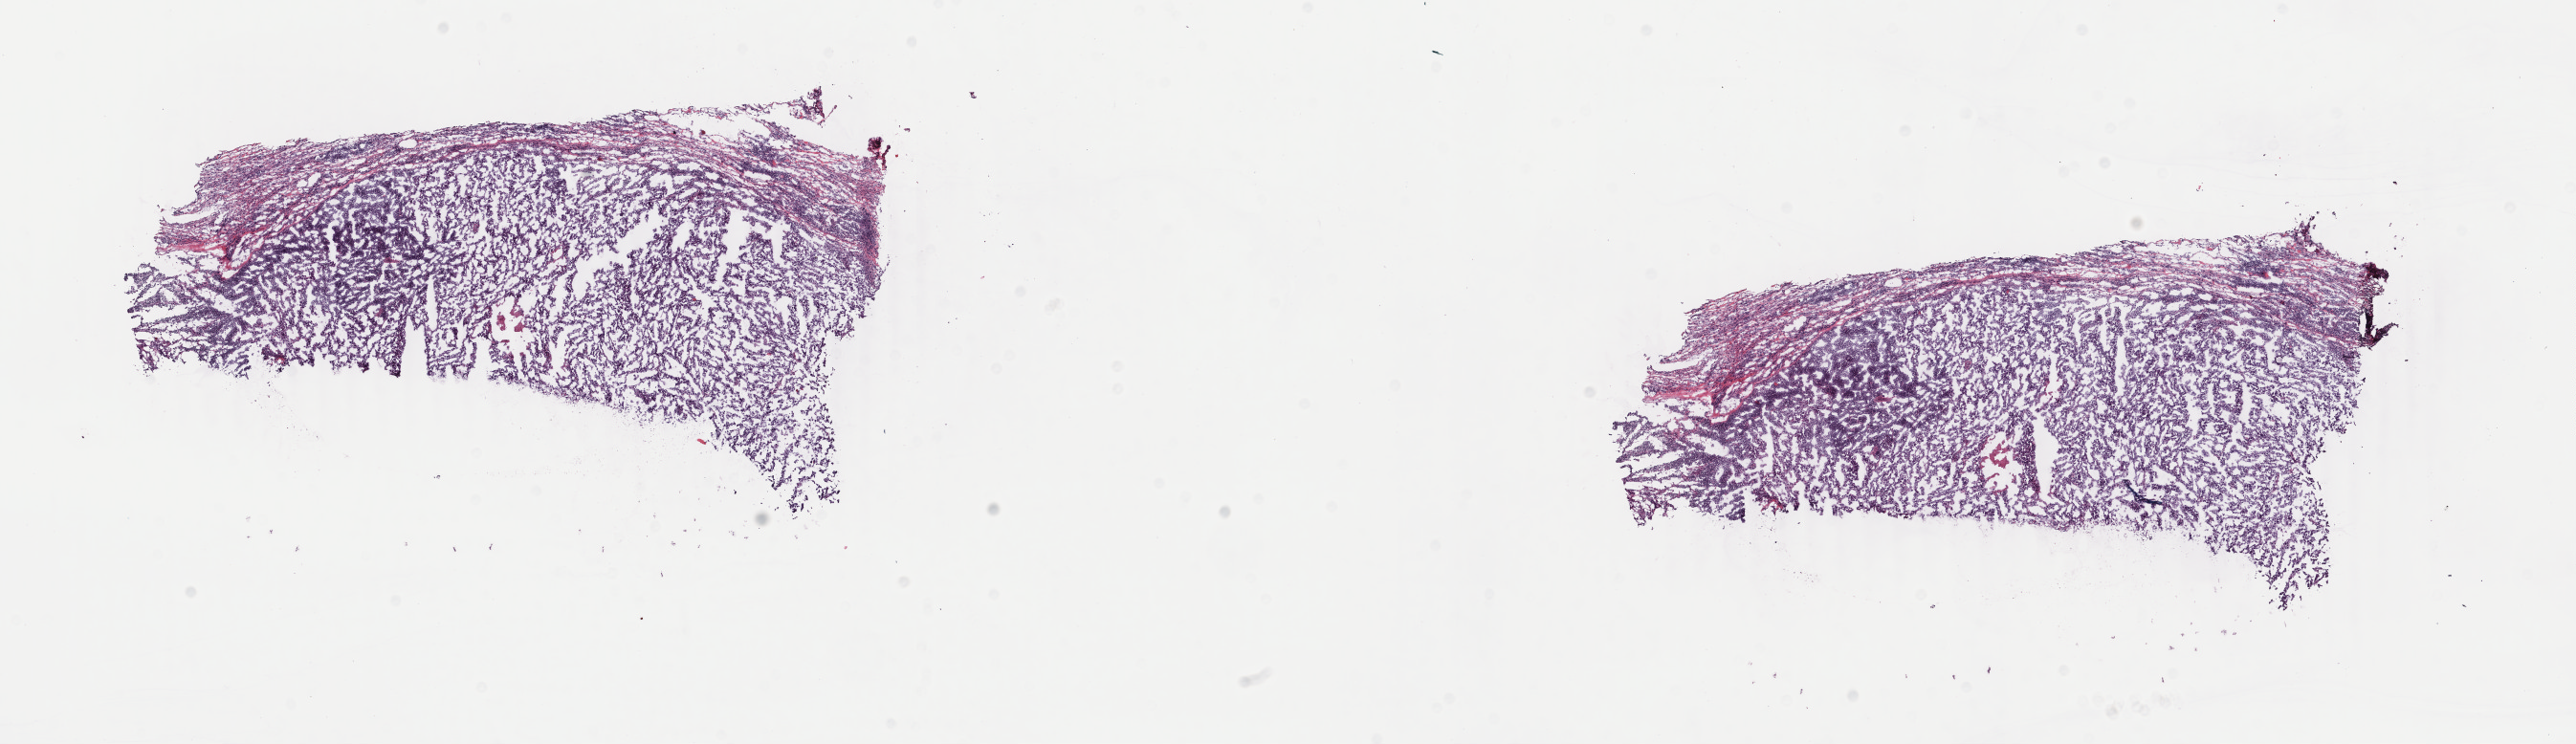
Digitized H&E-stained tissue section (whole slide) — shown as a low-resolution overview of the whole scanned area (about 21.4 x 6.2 mm, acquisition: 40x scan); frozen section from the top of the tissue portion; metastatic tumour sample, sampled site: lymph nodes of axilla or arm. Male patient; age at initial diagnosis 71 years. Pathologist review of this section (percent, as recorded): tumour cells 97%, tumour nuclei 80%, normal cells 0%, stromal cells 0%, necrosis 3%. Inflammatory infiltration, as recorded: lymphocyte infiltration 2%, monocyte infiltration 0%, neutrophil infiltration 0%.
This section: metastatic tumour tissue. Patient diagnosis: Malignant melanoma, NOS.